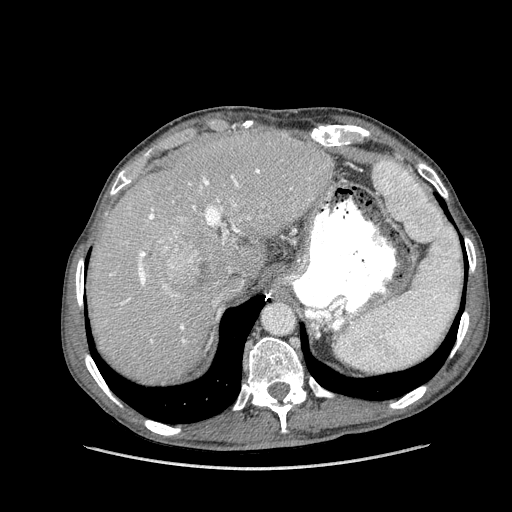
Contrast-enhanced abdominal CT (liver protocol), one axial slice. Position 113 of 162 along the scan axis. 100 kVp. Soft-tissue window (W 400 / L 40 HU). 512 × 512 image matrix, field of view 400 × 400 mm. From the clinical record (not read from this slice): diagnosis: hepatocellular carcinoma (patient treated with transarterial chemoembolisation; whether this scan precedes or follows treatment is not stated here); TNM stage (as recorded): Stage-IIIA; Child-Pugh class: A; tumour nodularity: multinodular.
Outlined on this slice (semi-automatic segmentation, software-assisted and operator-edited):
- abdominal aorta: box from (x=262, y=302) to (x=293, y=334) px
- liver parenchyma outside the tumour (the mass and vessels are separate outlines, so this box may not span the whole liver): (x=88, y=130)–(x=334, y=382)
- mass: (x=165, y=244)–(x=236, y=303)
- liver vessels: (x=110, y=169)–(x=292, y=343)